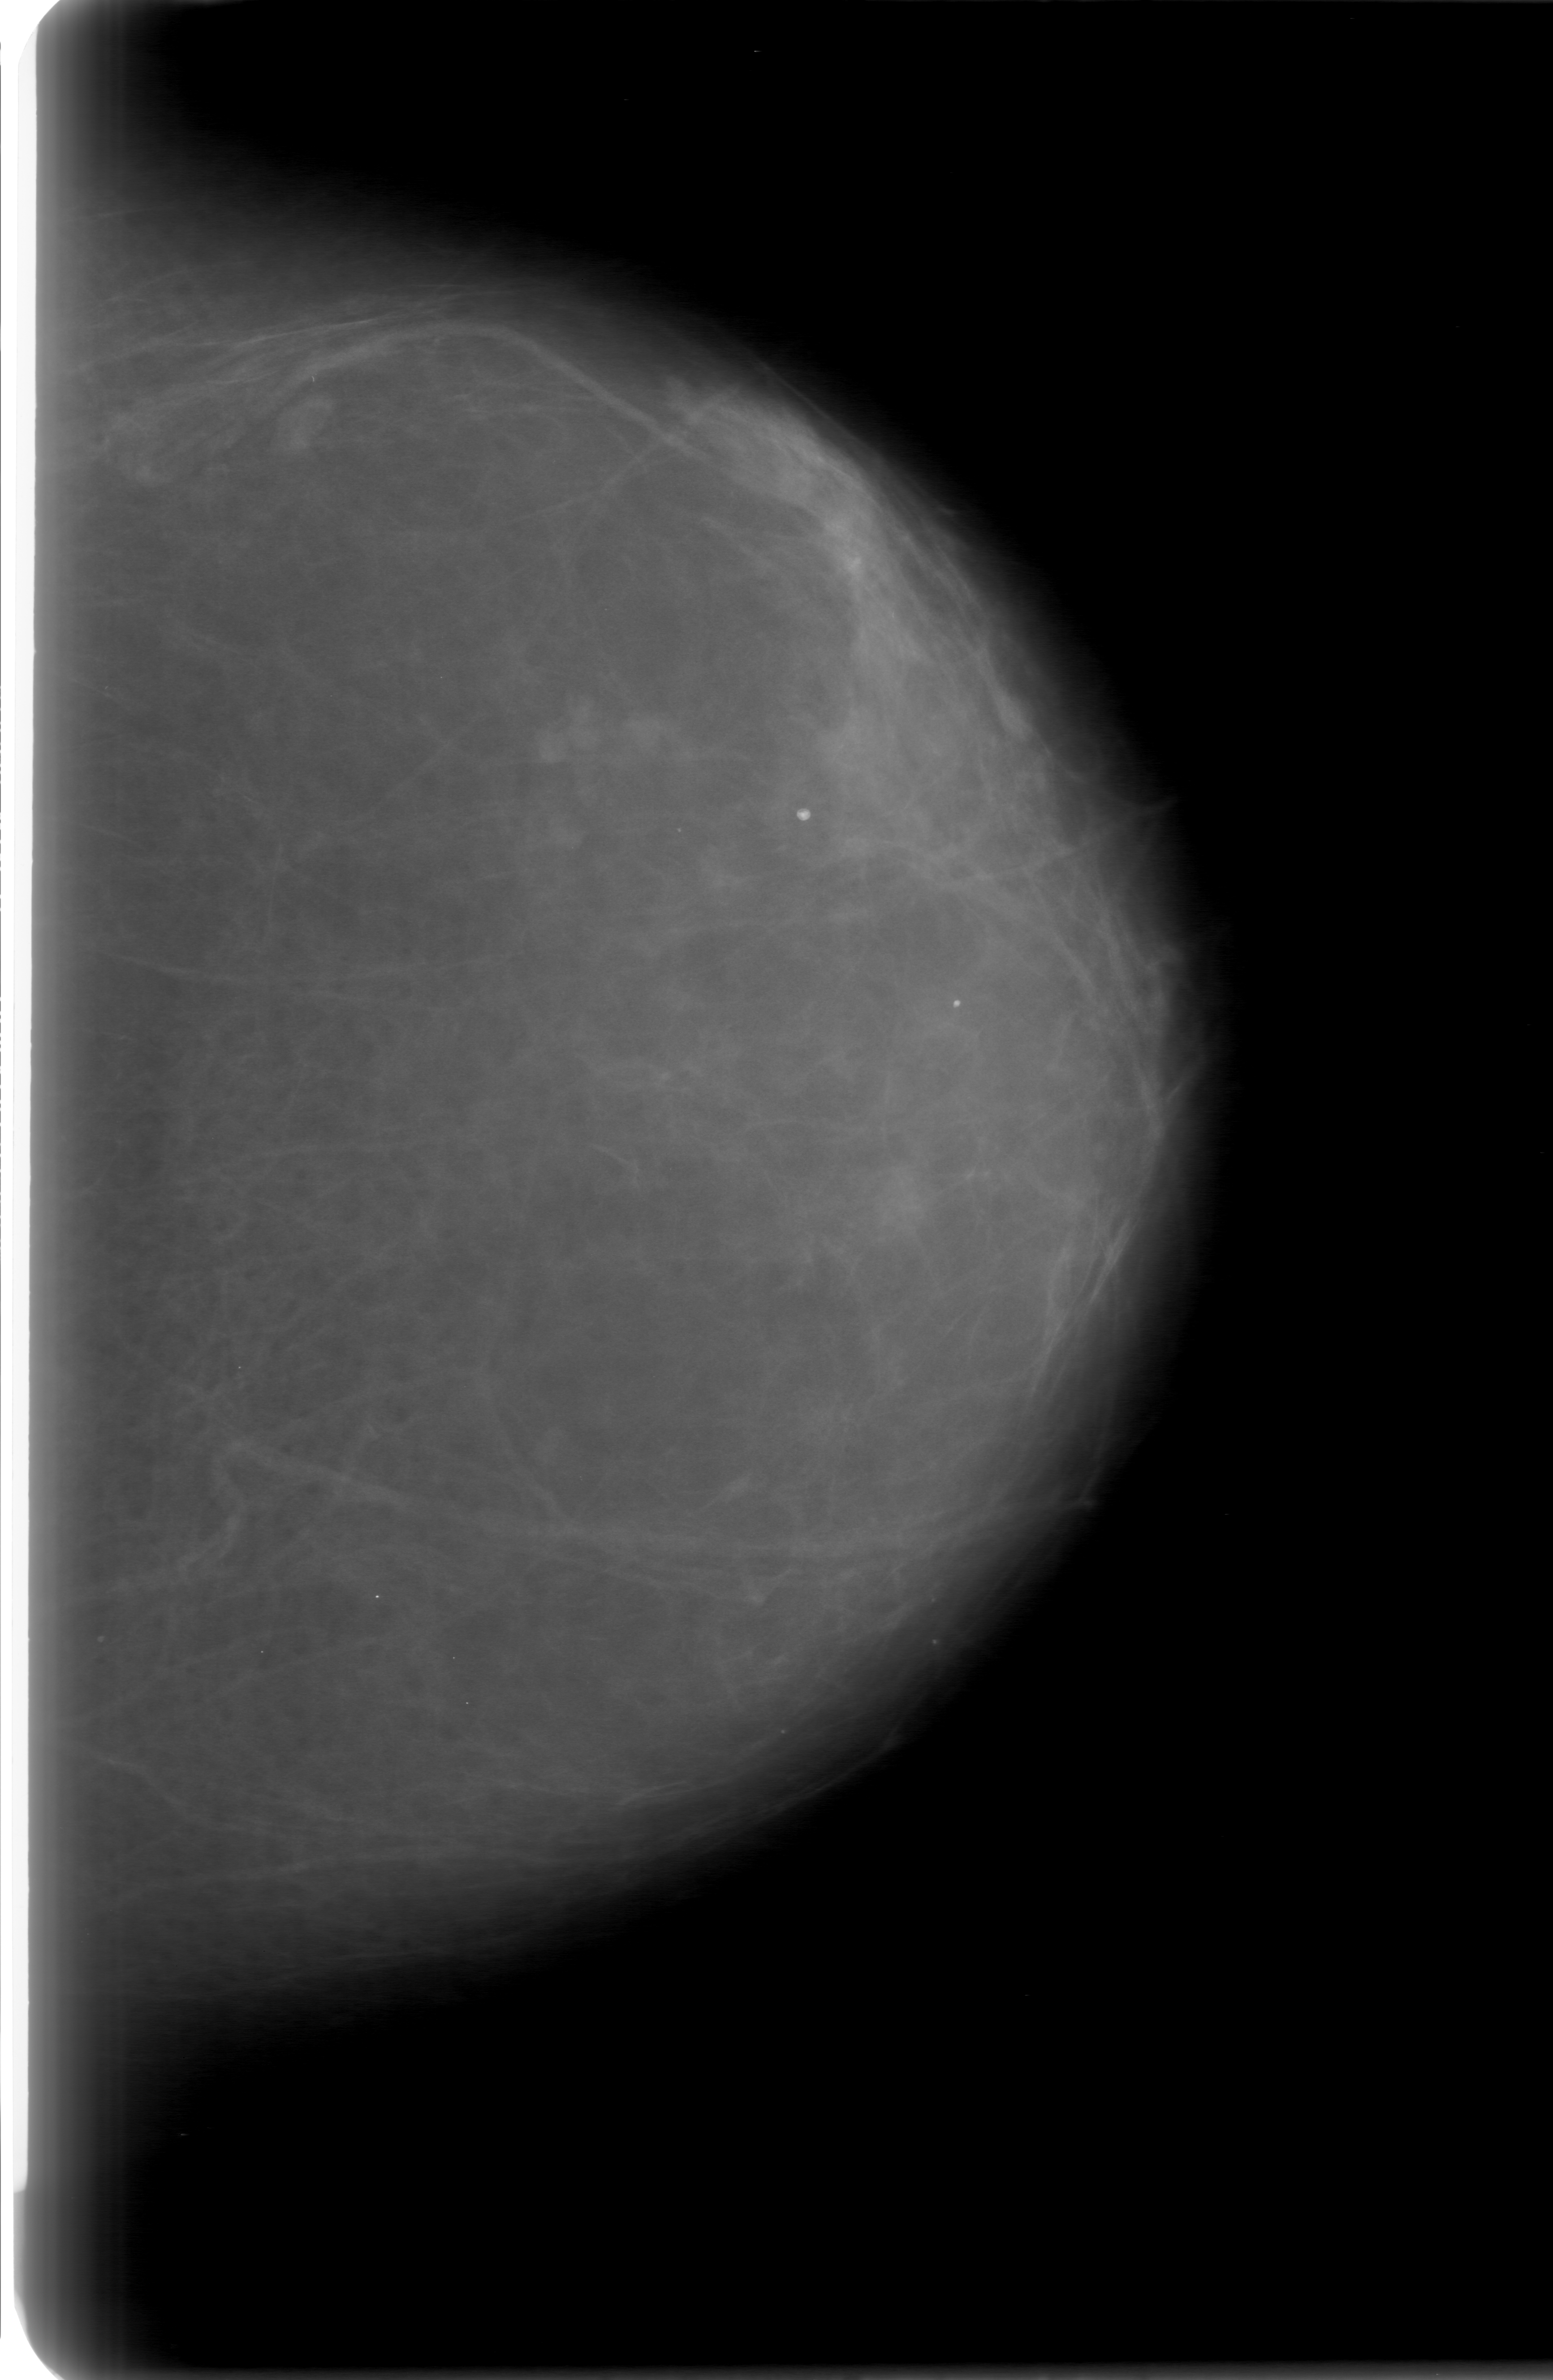
Digitized screen-film mammogram; left breast; CC view; BI-RADS breast density category 1 (scale 1–4); 1553 × 2380 image matrix.
Marked abnormalities (boxes around the expert regions of interest):
- mass, shape lobulated, margins obscured; BI-RADS assessment category 0 (incomplete: needs additional imaging); subtlety rating 2 on a 1 (subtle) to 5 (obvious) scale; pathology (as recorded): benign: bounding box <785,677,919,837> (left, top, right, bottom; pixels)